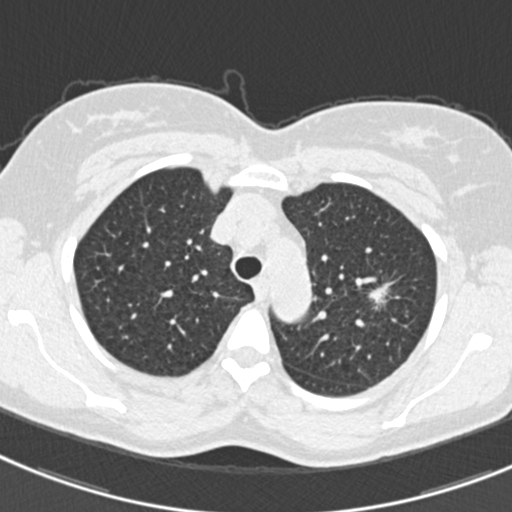
Low-dose screening chest CT, one axial slice. Position 244 of 309 along the scan axis. 120 kVp. Lung window (W 1500 / L -600 HU). 1 mm slice thickness. 512 × 512 image matrix, field of view 302 × 302 mm.
Outlined on this slice (outlined manually by an expert reader):
- lesion 1 (tumor, upper lobe of left lung): bounding box (x1, y1, x2, y2) in pixels: (369, 286, 388, 304)